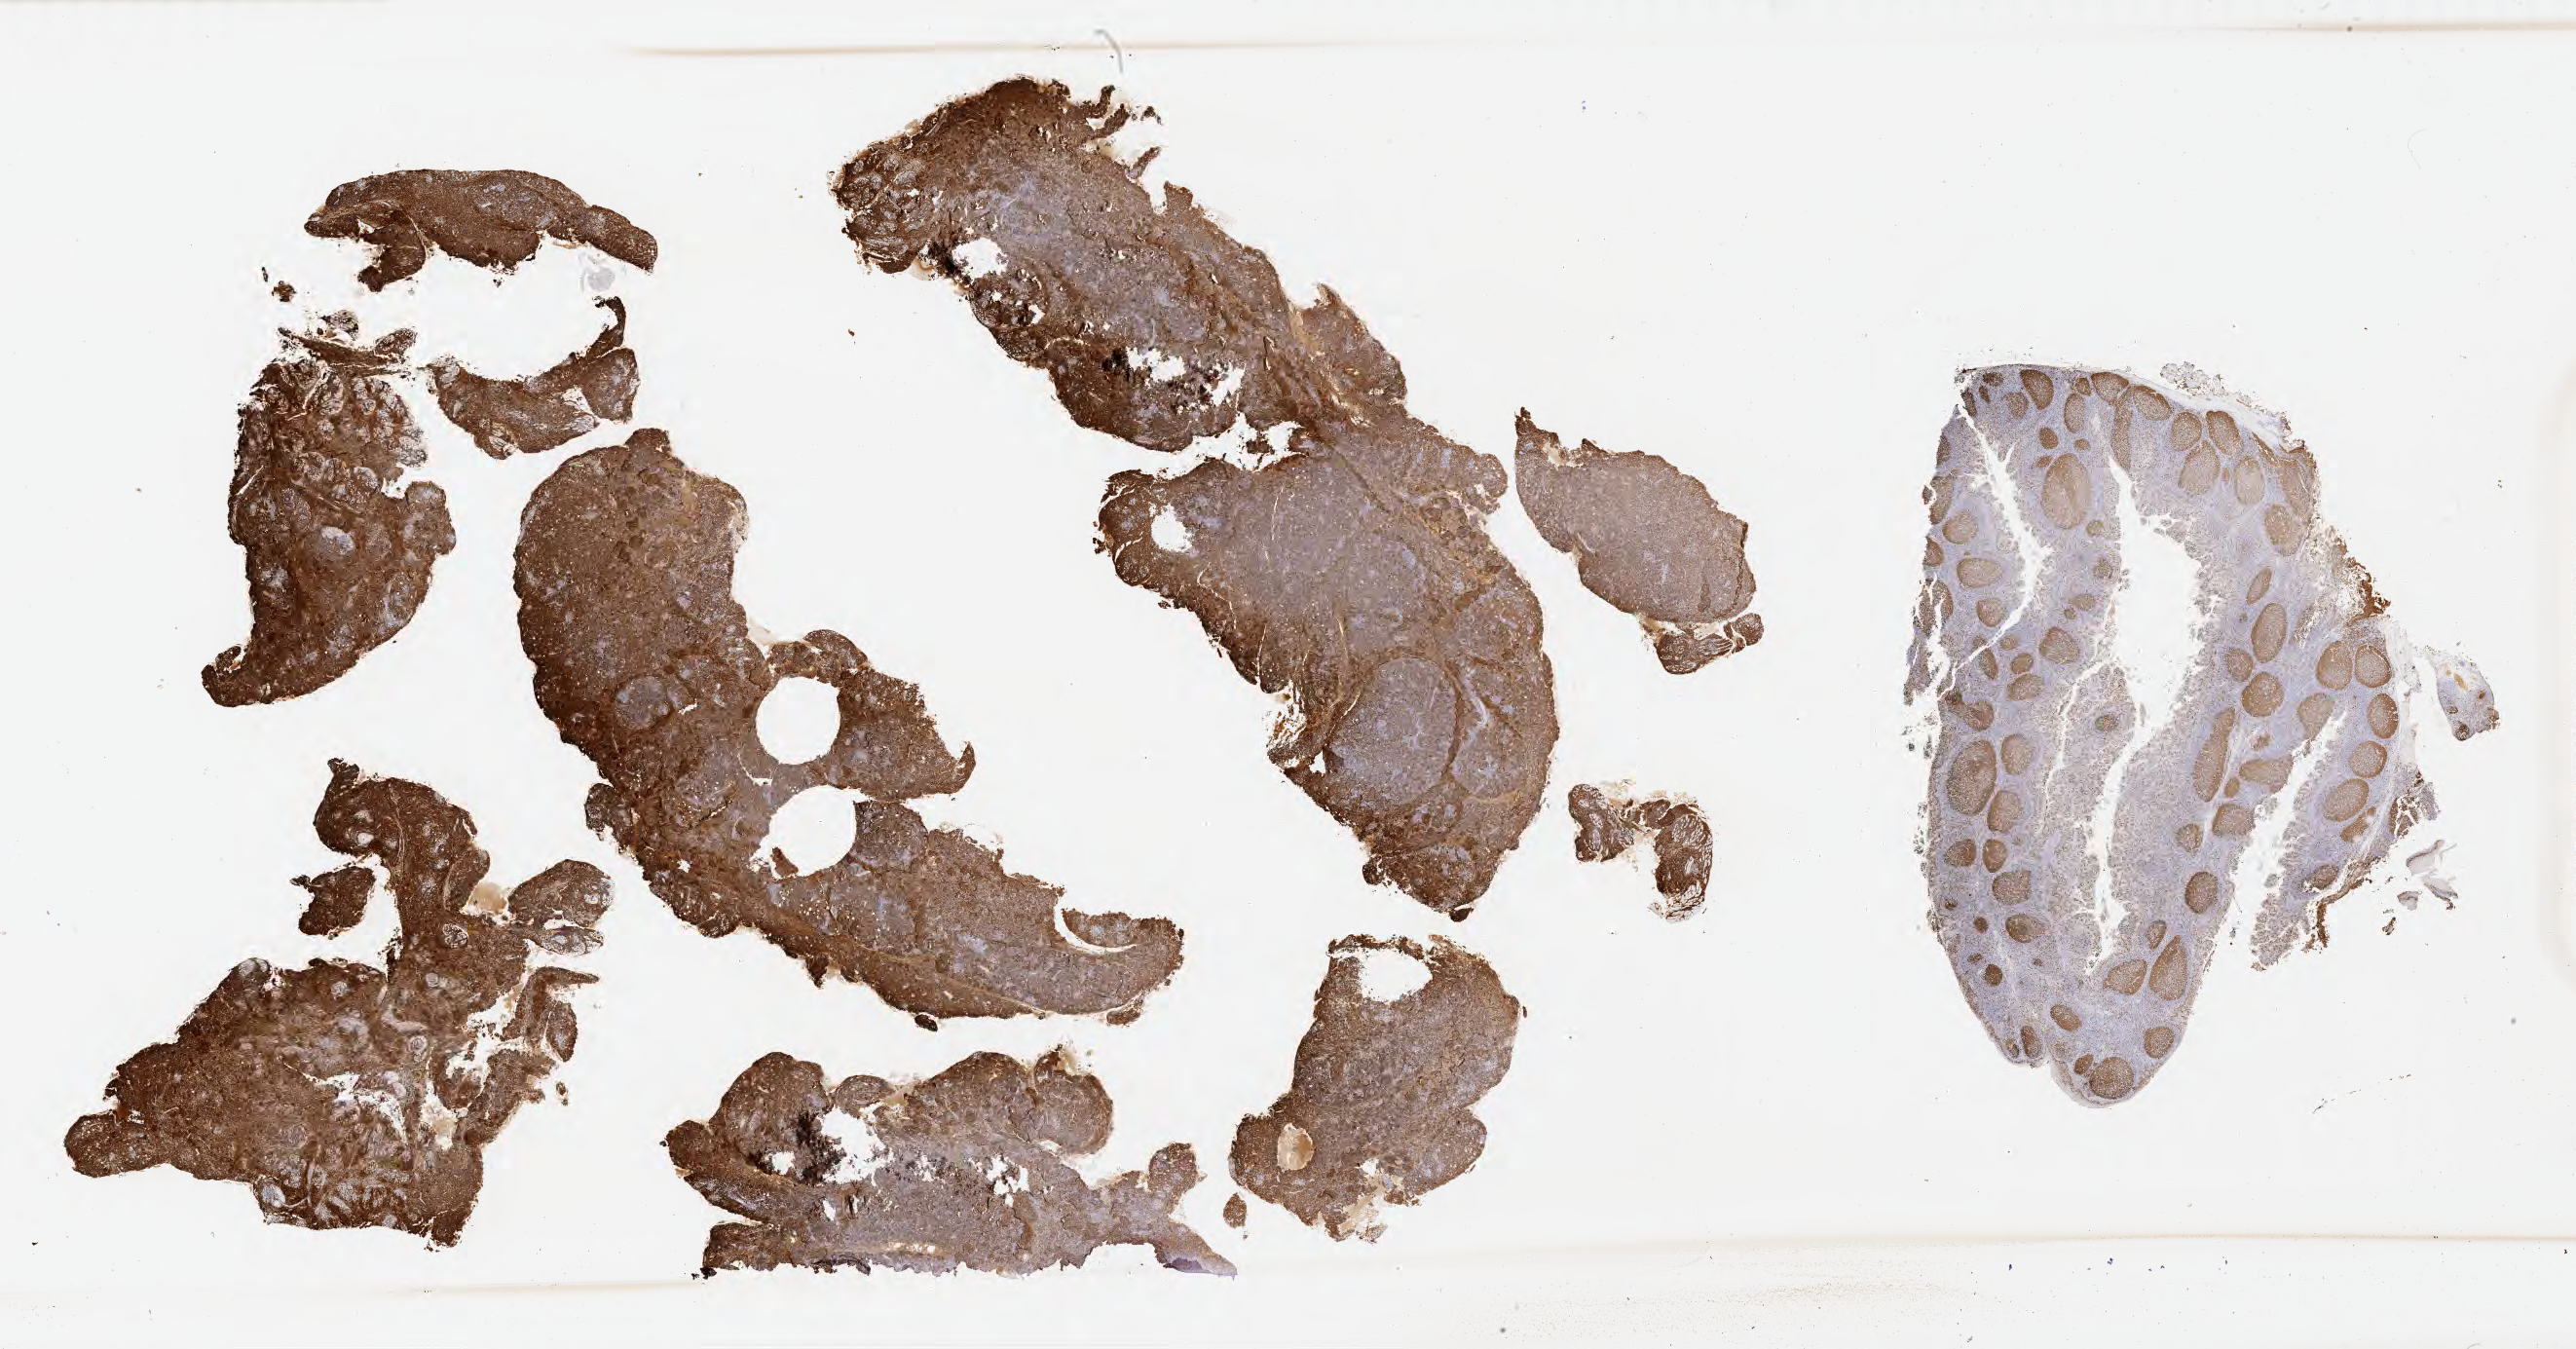
Immunohistochemistry (IHC) whole-slide image stained for Ki-67, a low-resolution overview of the entire scanned area, about 42.8 x 22.4 mm, tumor tissue, anatomic site: cranium. Patient: male, age at initial diagnosis 5 years.
- diagnosis: Burkitt lymphoma, NOS